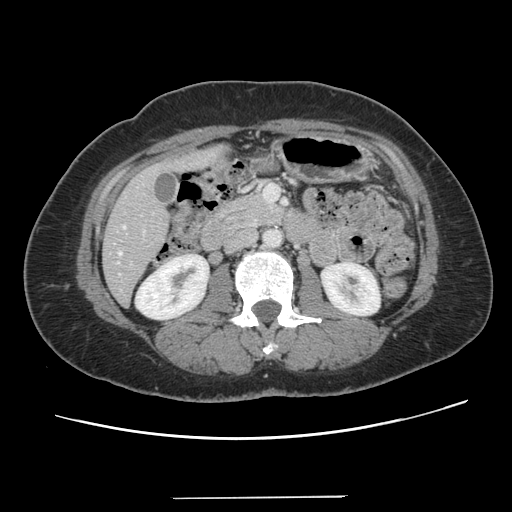
Contrast-enhanced abdominal CT, one axial slice. Slice 45 of 141 in the series (ordered by position). 120 kVp. Intravenous contrast given. Soft-tissue window (W 400 / L 40 HU). 512 × 512 image matrix, field of view 366 × 366 mm. Female patient, age 53 years. From the clinical record (not read from this slice): diagnosis: colorectal cancer liver metastases, imaged before liver resection; multiple liver metastases: no.
Annotated regions visible in this slice (manually delineated by an expert):
- hepatic veins: bounding box <118,226,125,254> (left, top, right, bottom; pixels)
- liver: <104,148,225,304>
- planned liver remnant (the part of the liver to remain after resection): <104,217,169,304>